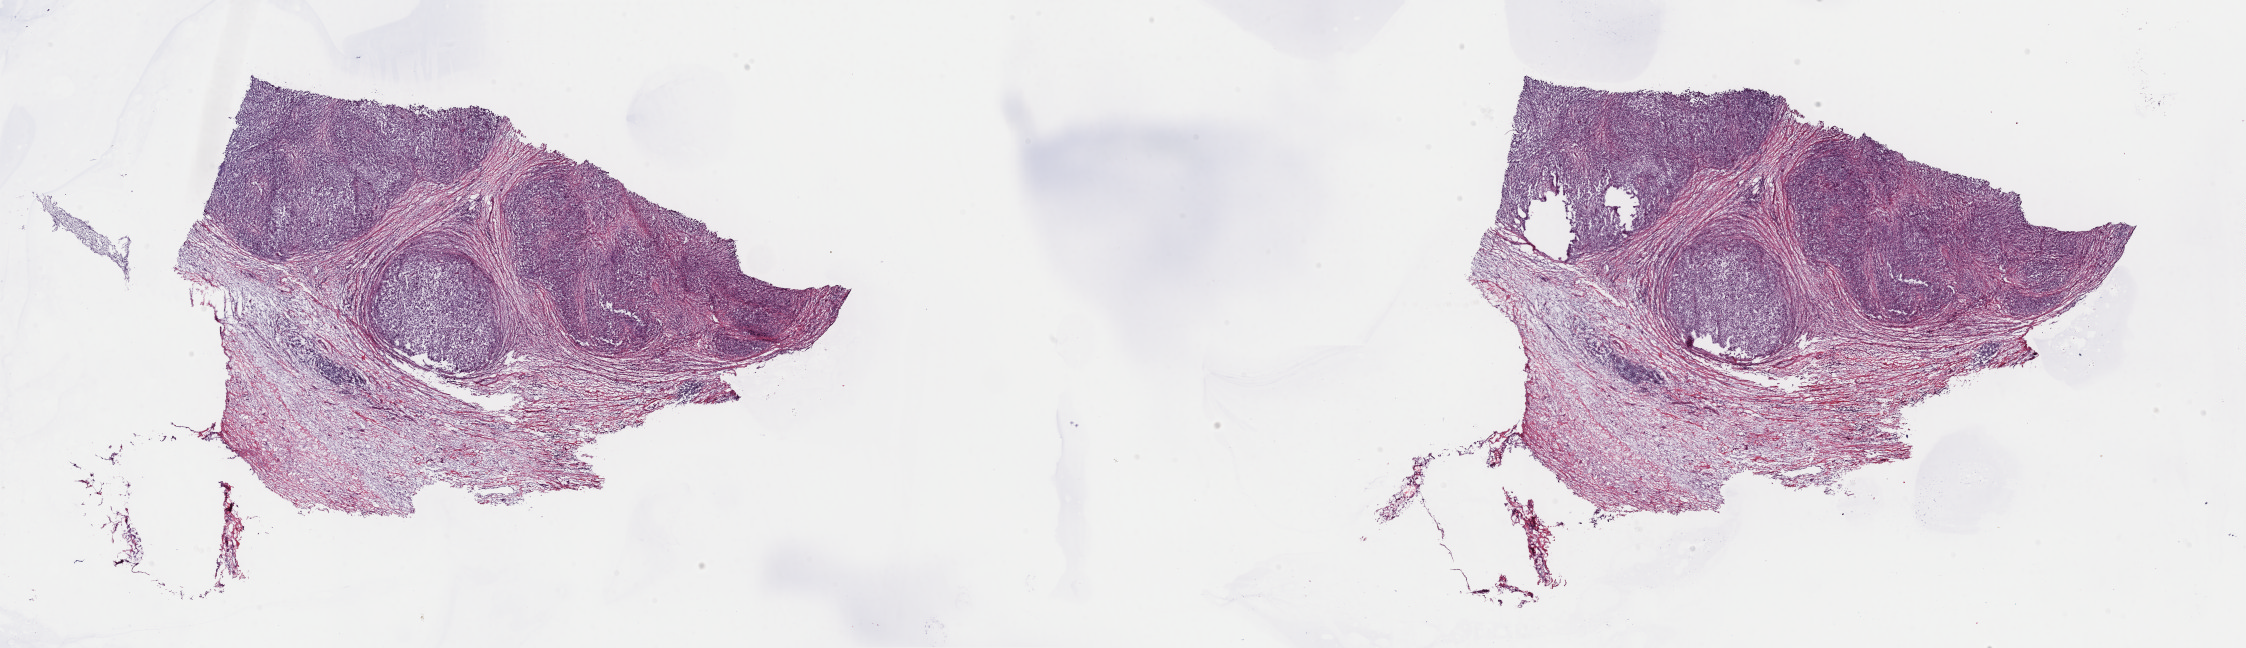
H&E whole-slide image — a low-resolution overview of the entire scanned area, about 35.5 x 10.2 mm (acquisition: 40x scan); frozen section from the top of the tissue portion; metastatic tumour sample, sampled site: lymph nodes of inguinal region or leg. Patient: male, age at initial diagnosis 51 years. Composition of this section per pathologist review: tumour cells 70%, tumour nuclei 70%, normal cells 30%, stromal cells 0%, necrosis 0%. Infiltration values recorded for this section: lymphocyte infiltration 5%, monocyte infiltration 0%, neutrophil infiltration 0%.
This section: metastatic tumour tissue. Patient diagnosis: Nodular melanoma.